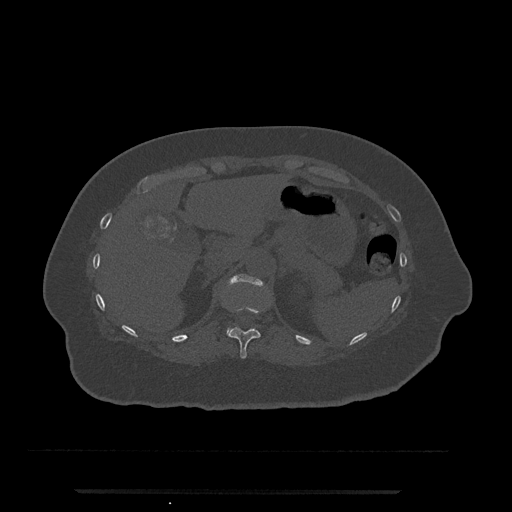
CT including the spine, one axial slice. Slice 208 of 797 in the series (ordered by position). Reconstruction kernel Br40s/3. 120 kVp. Bone window (W 1800 / L 400 HU). 0.5 mm slice thickness. 512 × 512 image matrix, field of view 440 × 440 mm. Patient: female, 51 years. Case-level facts recorded for this patient, not image findings: primary cancer: neuro.
Outlined on this slice (semi-automatic segmentation, software-assisted and operator-edited):
- T11 vertebra: bounding box (x1, y1, x2, y2) in pixels: (228, 307, 261, 359)
- T12 vertebra: (227, 274, 263, 334)